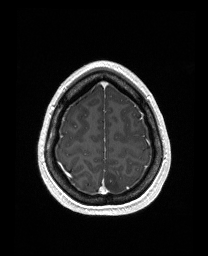
Brain MRI from a brain-tumour surgery series, one axial slice. Position 133 of 176 along the scan axis. T1-weighted post-contrast. 1 mm slice thickness. 208 × 256 image matrix, field of view 203 × 250 mm. Case-level facts recorded for this patient, not image findings: histopathology: Astrocytoma; WHO grade: 3; IDH mutation: yes; tumour location: Left Frontal.
Annotated regions visible in this slice (expert manual segmentation):
- tumour: bounding box (x1, y1, x2, y2) in pixels: (133, 134, 147, 144)